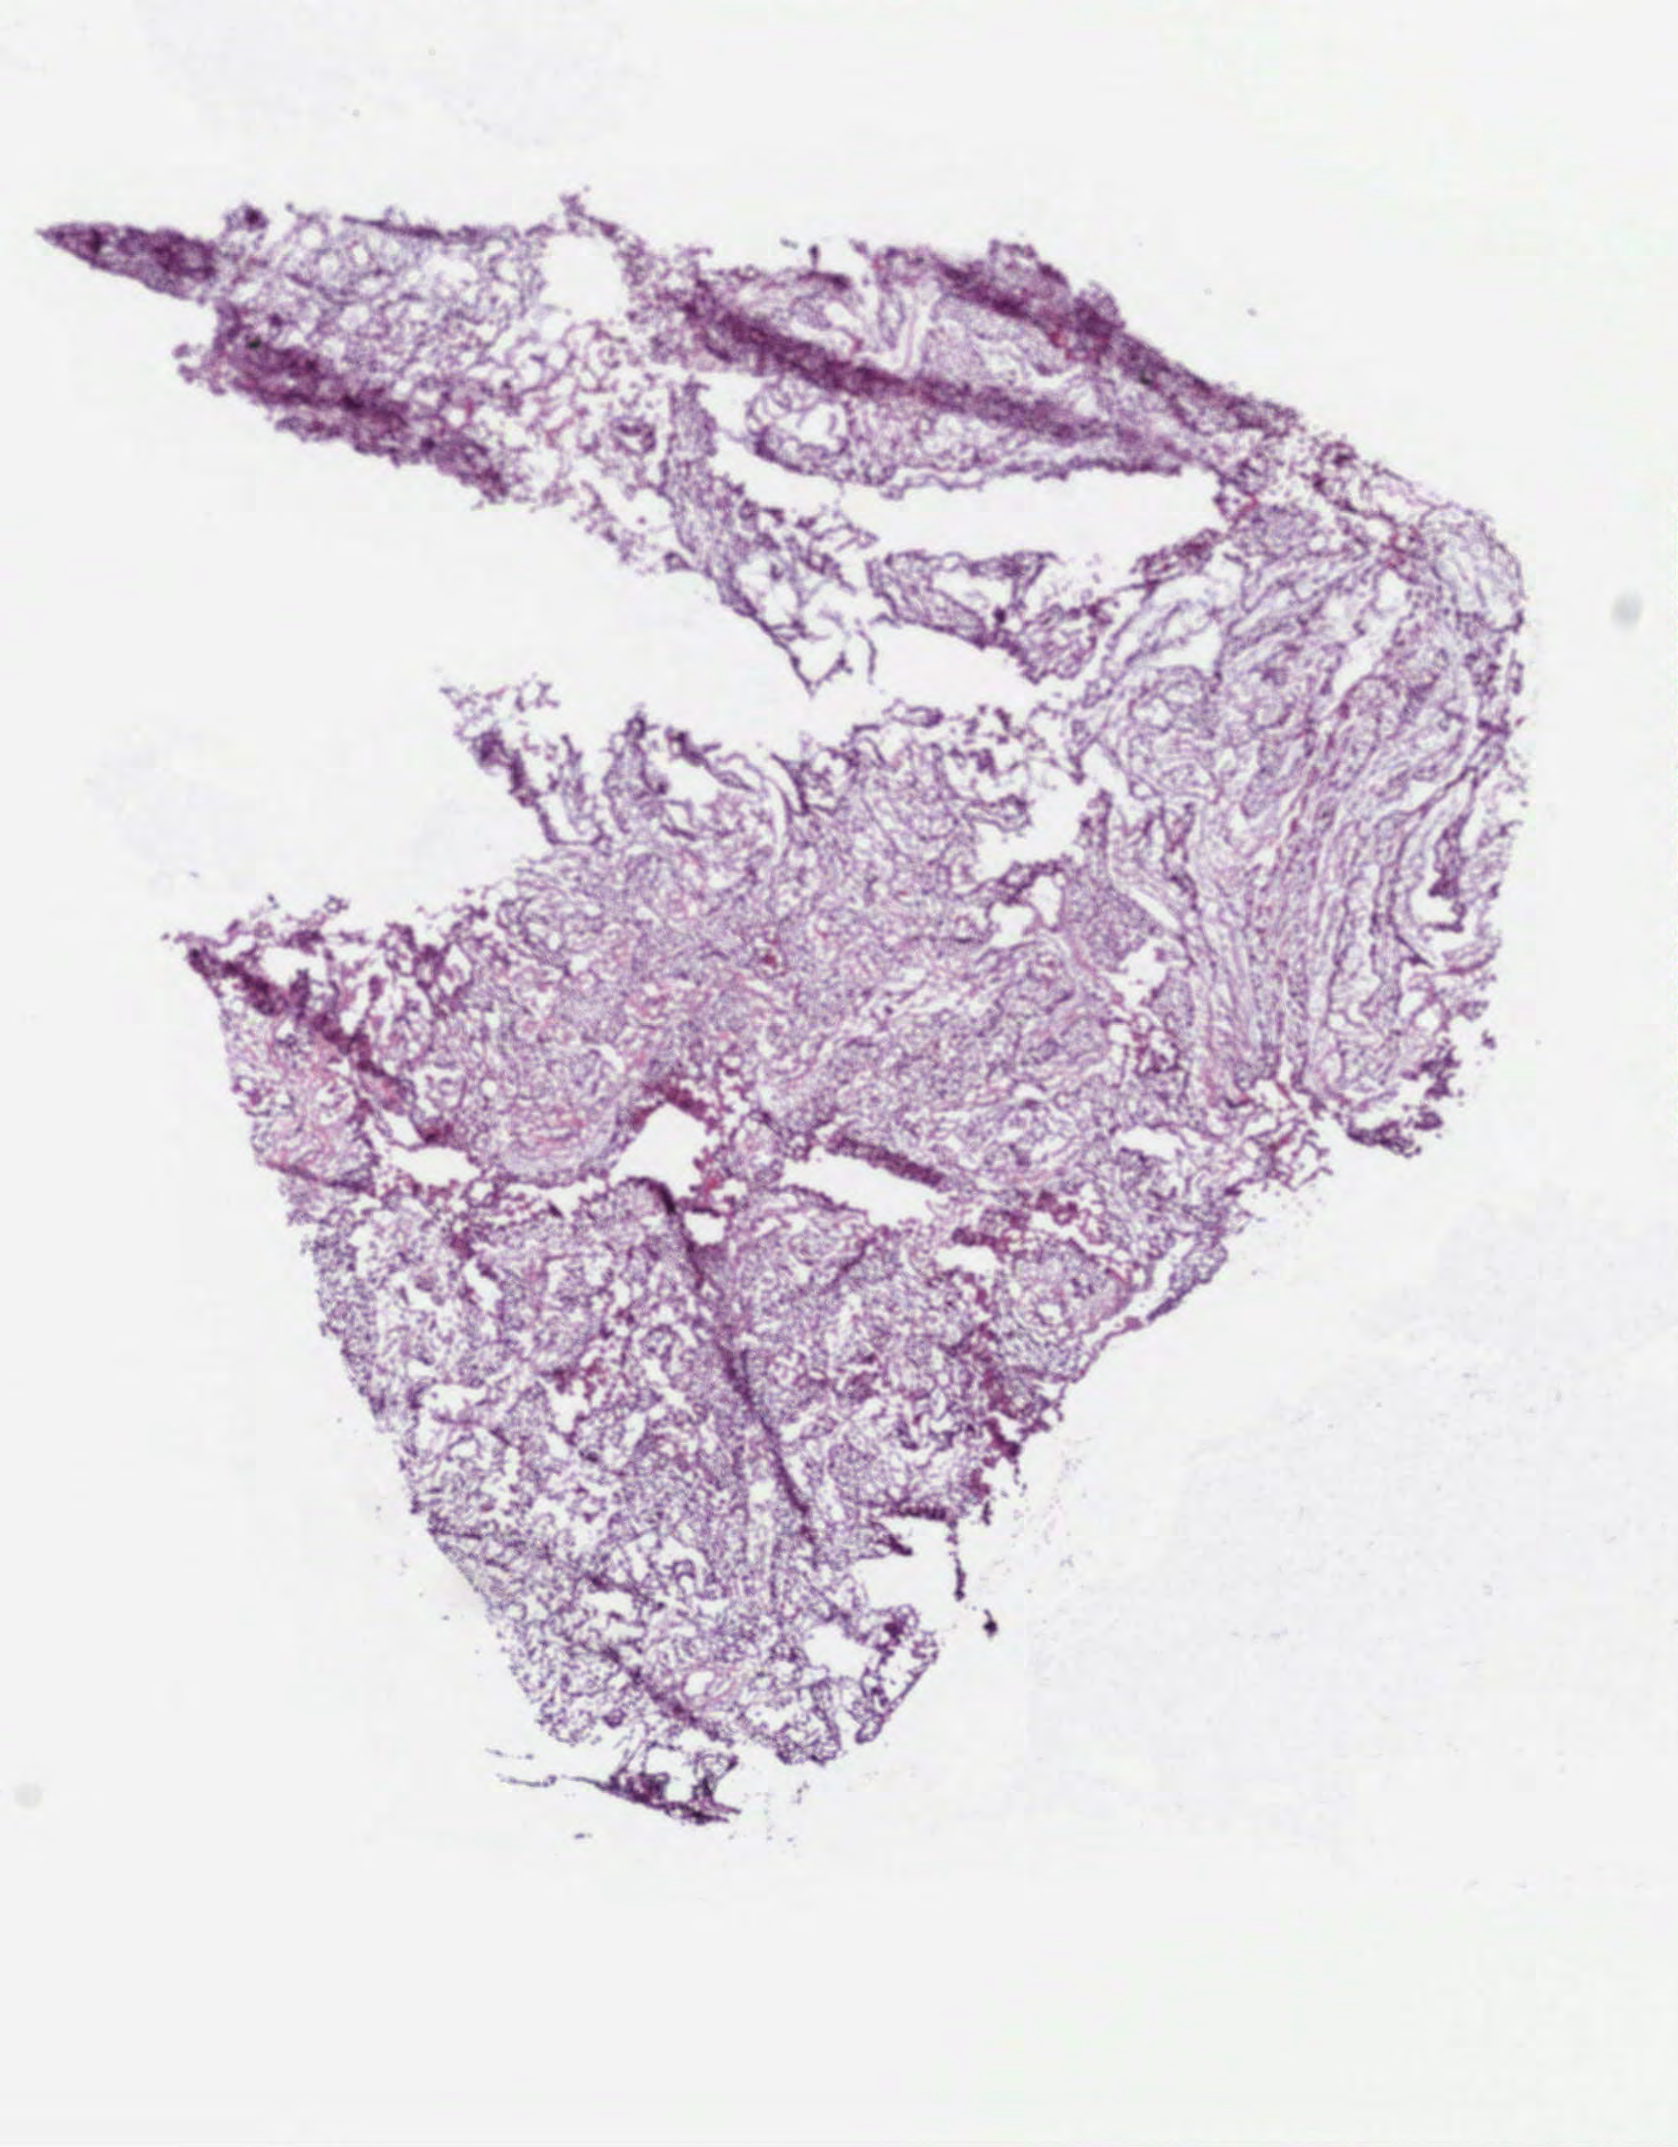
Whole-slide histology image, Hematoxylin and eosin (H&E) stained, low-resolution overview of the scanned area, about 6.8 x 8.7 mm; frozen section from the top of the tissue portion; primary tumour sample from the lung. Female patient; age at initial diagnosis 60 years. Composition of this section per pathologist review: tumour cells 80%, tumour nuclei 70%, normal cells 20%, stromal cells 0%, necrosis 0%.
Histologic diagnosis: Squamous cell carcinoma, NOS (overlapping lesion of lung). Laterality: right. AJCC pathologic stage: IIB (6th edition). TNM: T3 N0 M0.